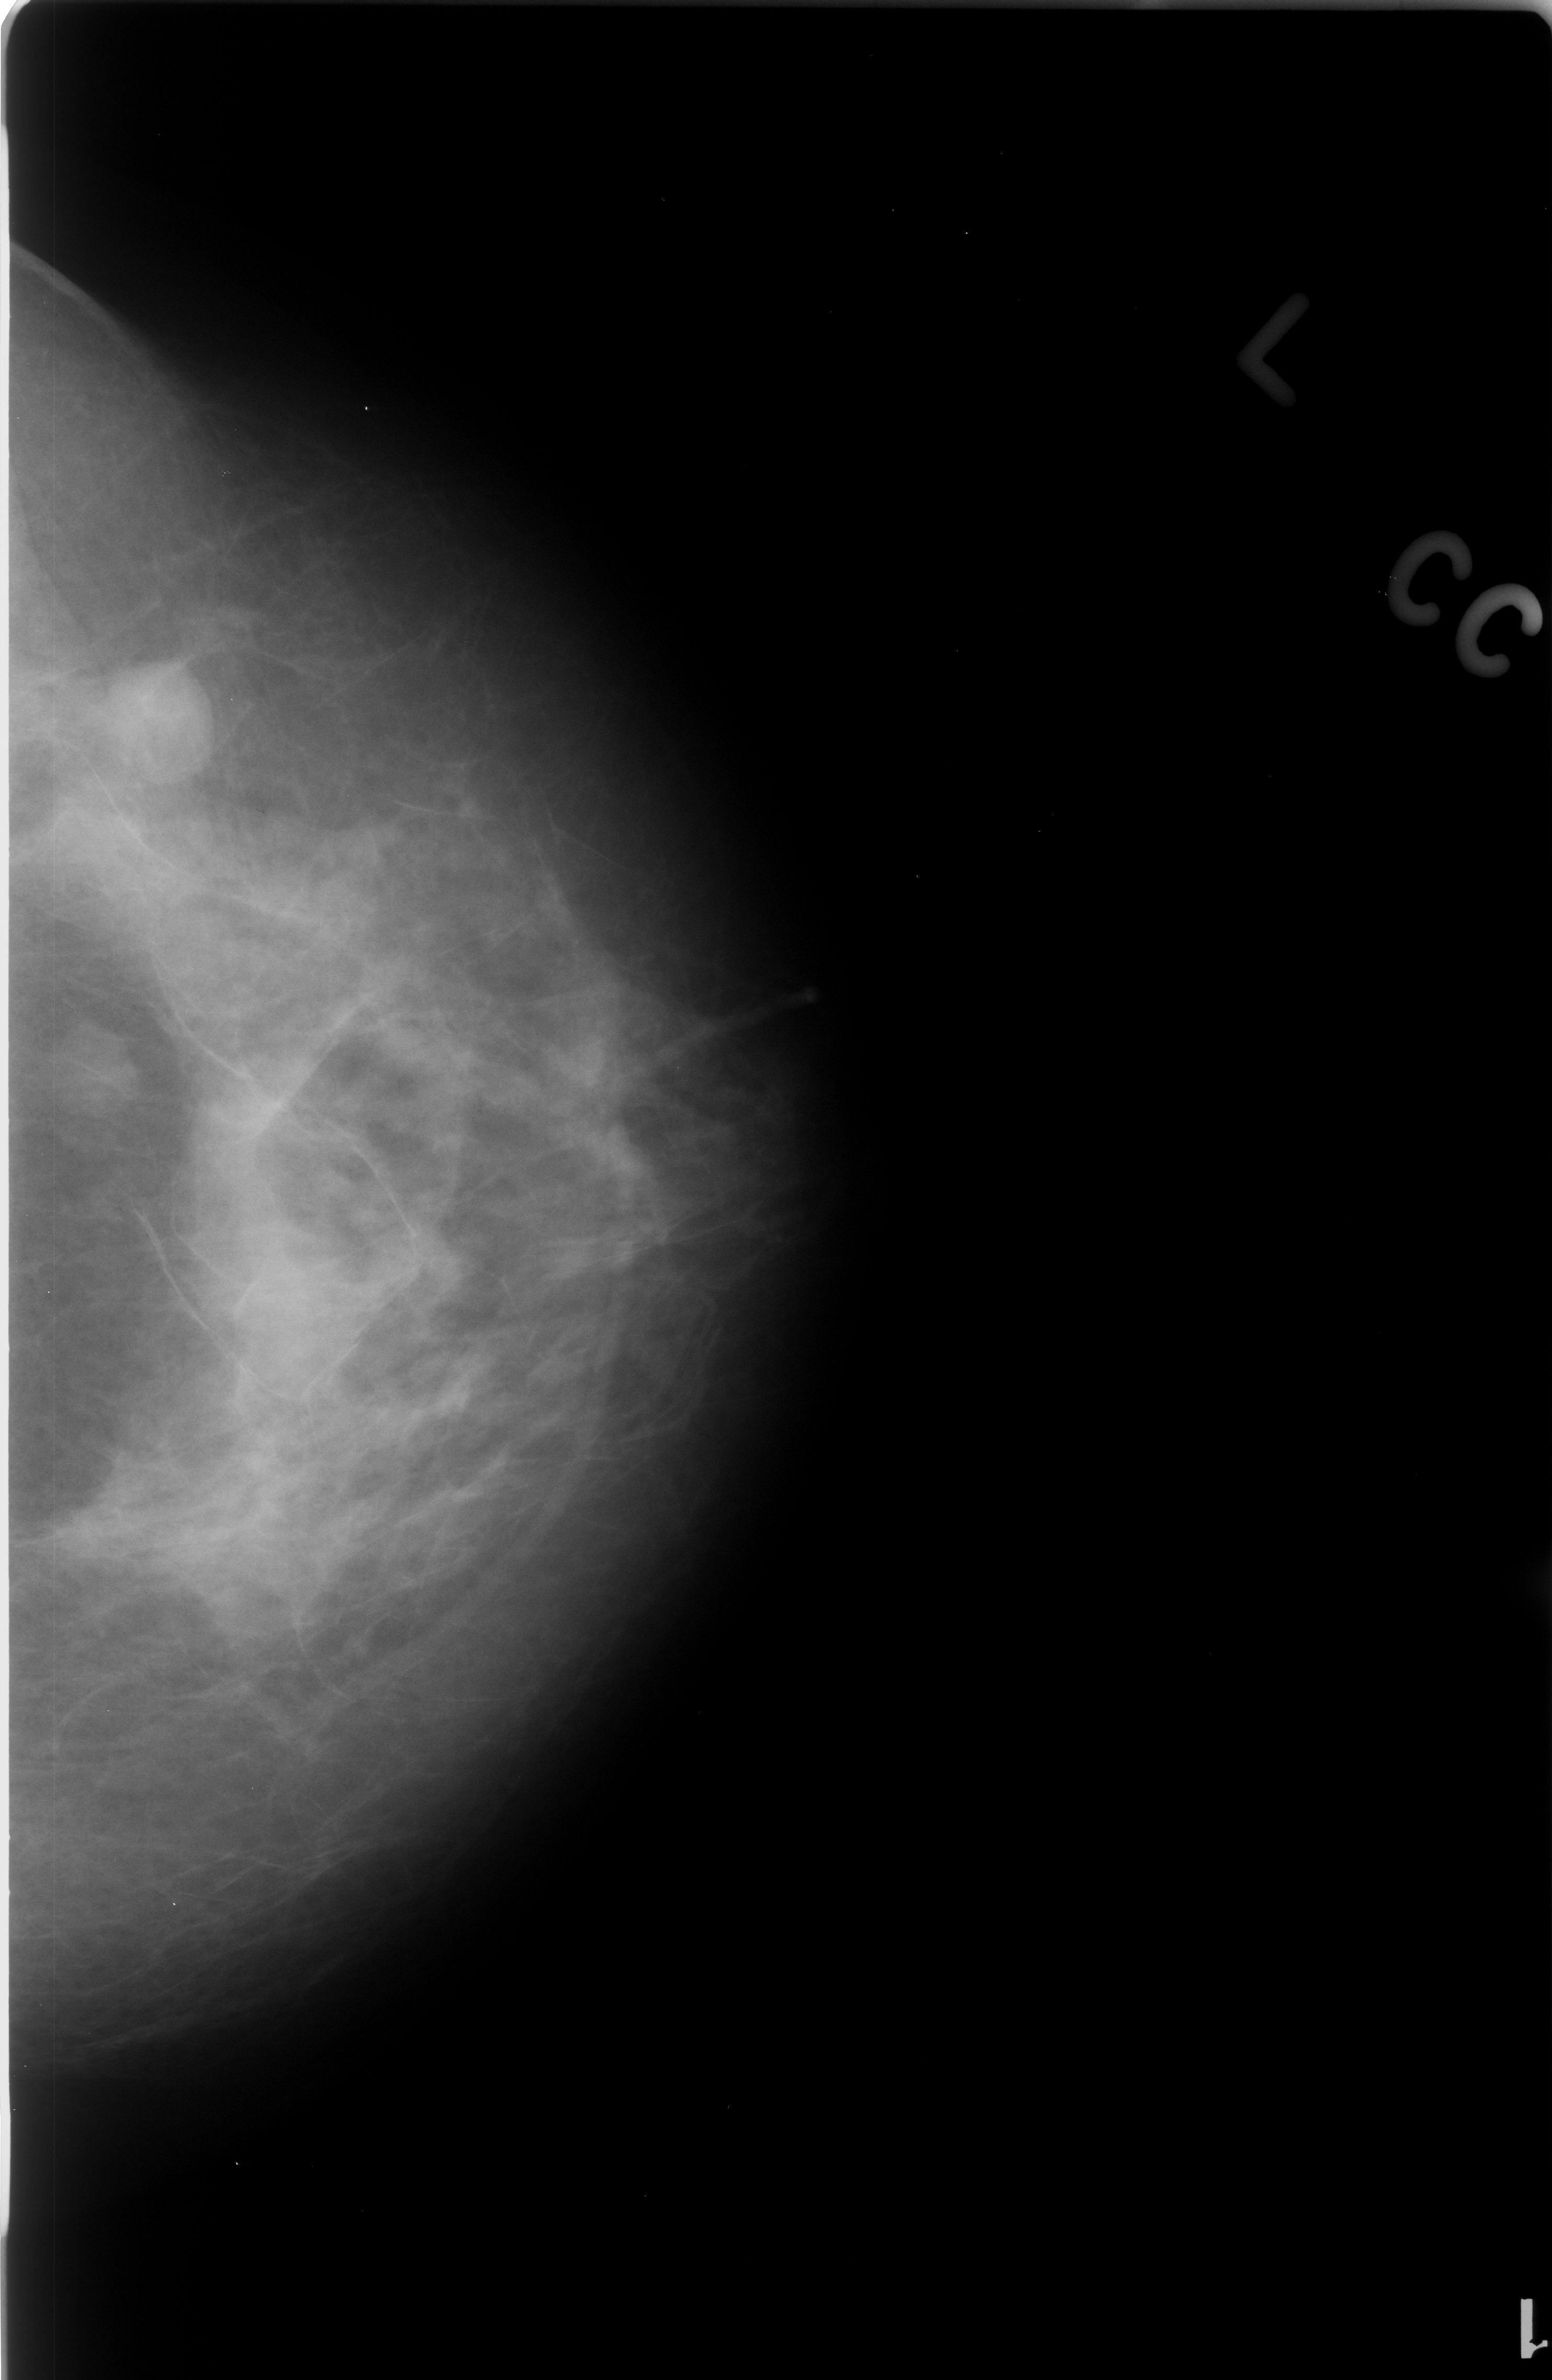
Digitized screen-film mammogram; left breast; craniocaudal (CC) view; 1552 × 2380 image matrix.
Expert-marked regions of interest on this image (one box per marked abnormality):
- Finding 1 of 2: mass, shape oval, margins circumscribed; BI-RADS assessment category 3; pathology (as recorded): benign: box from (x=47, y=1019) to (x=144, y=1119) px
- Finding 2 of 2: mass, shape oval, margins circumscribed; BI-RADS assessment category 3; pathology result (as recorded, not read from the image): benign: (x=82, y=645)–(x=224, y=786)